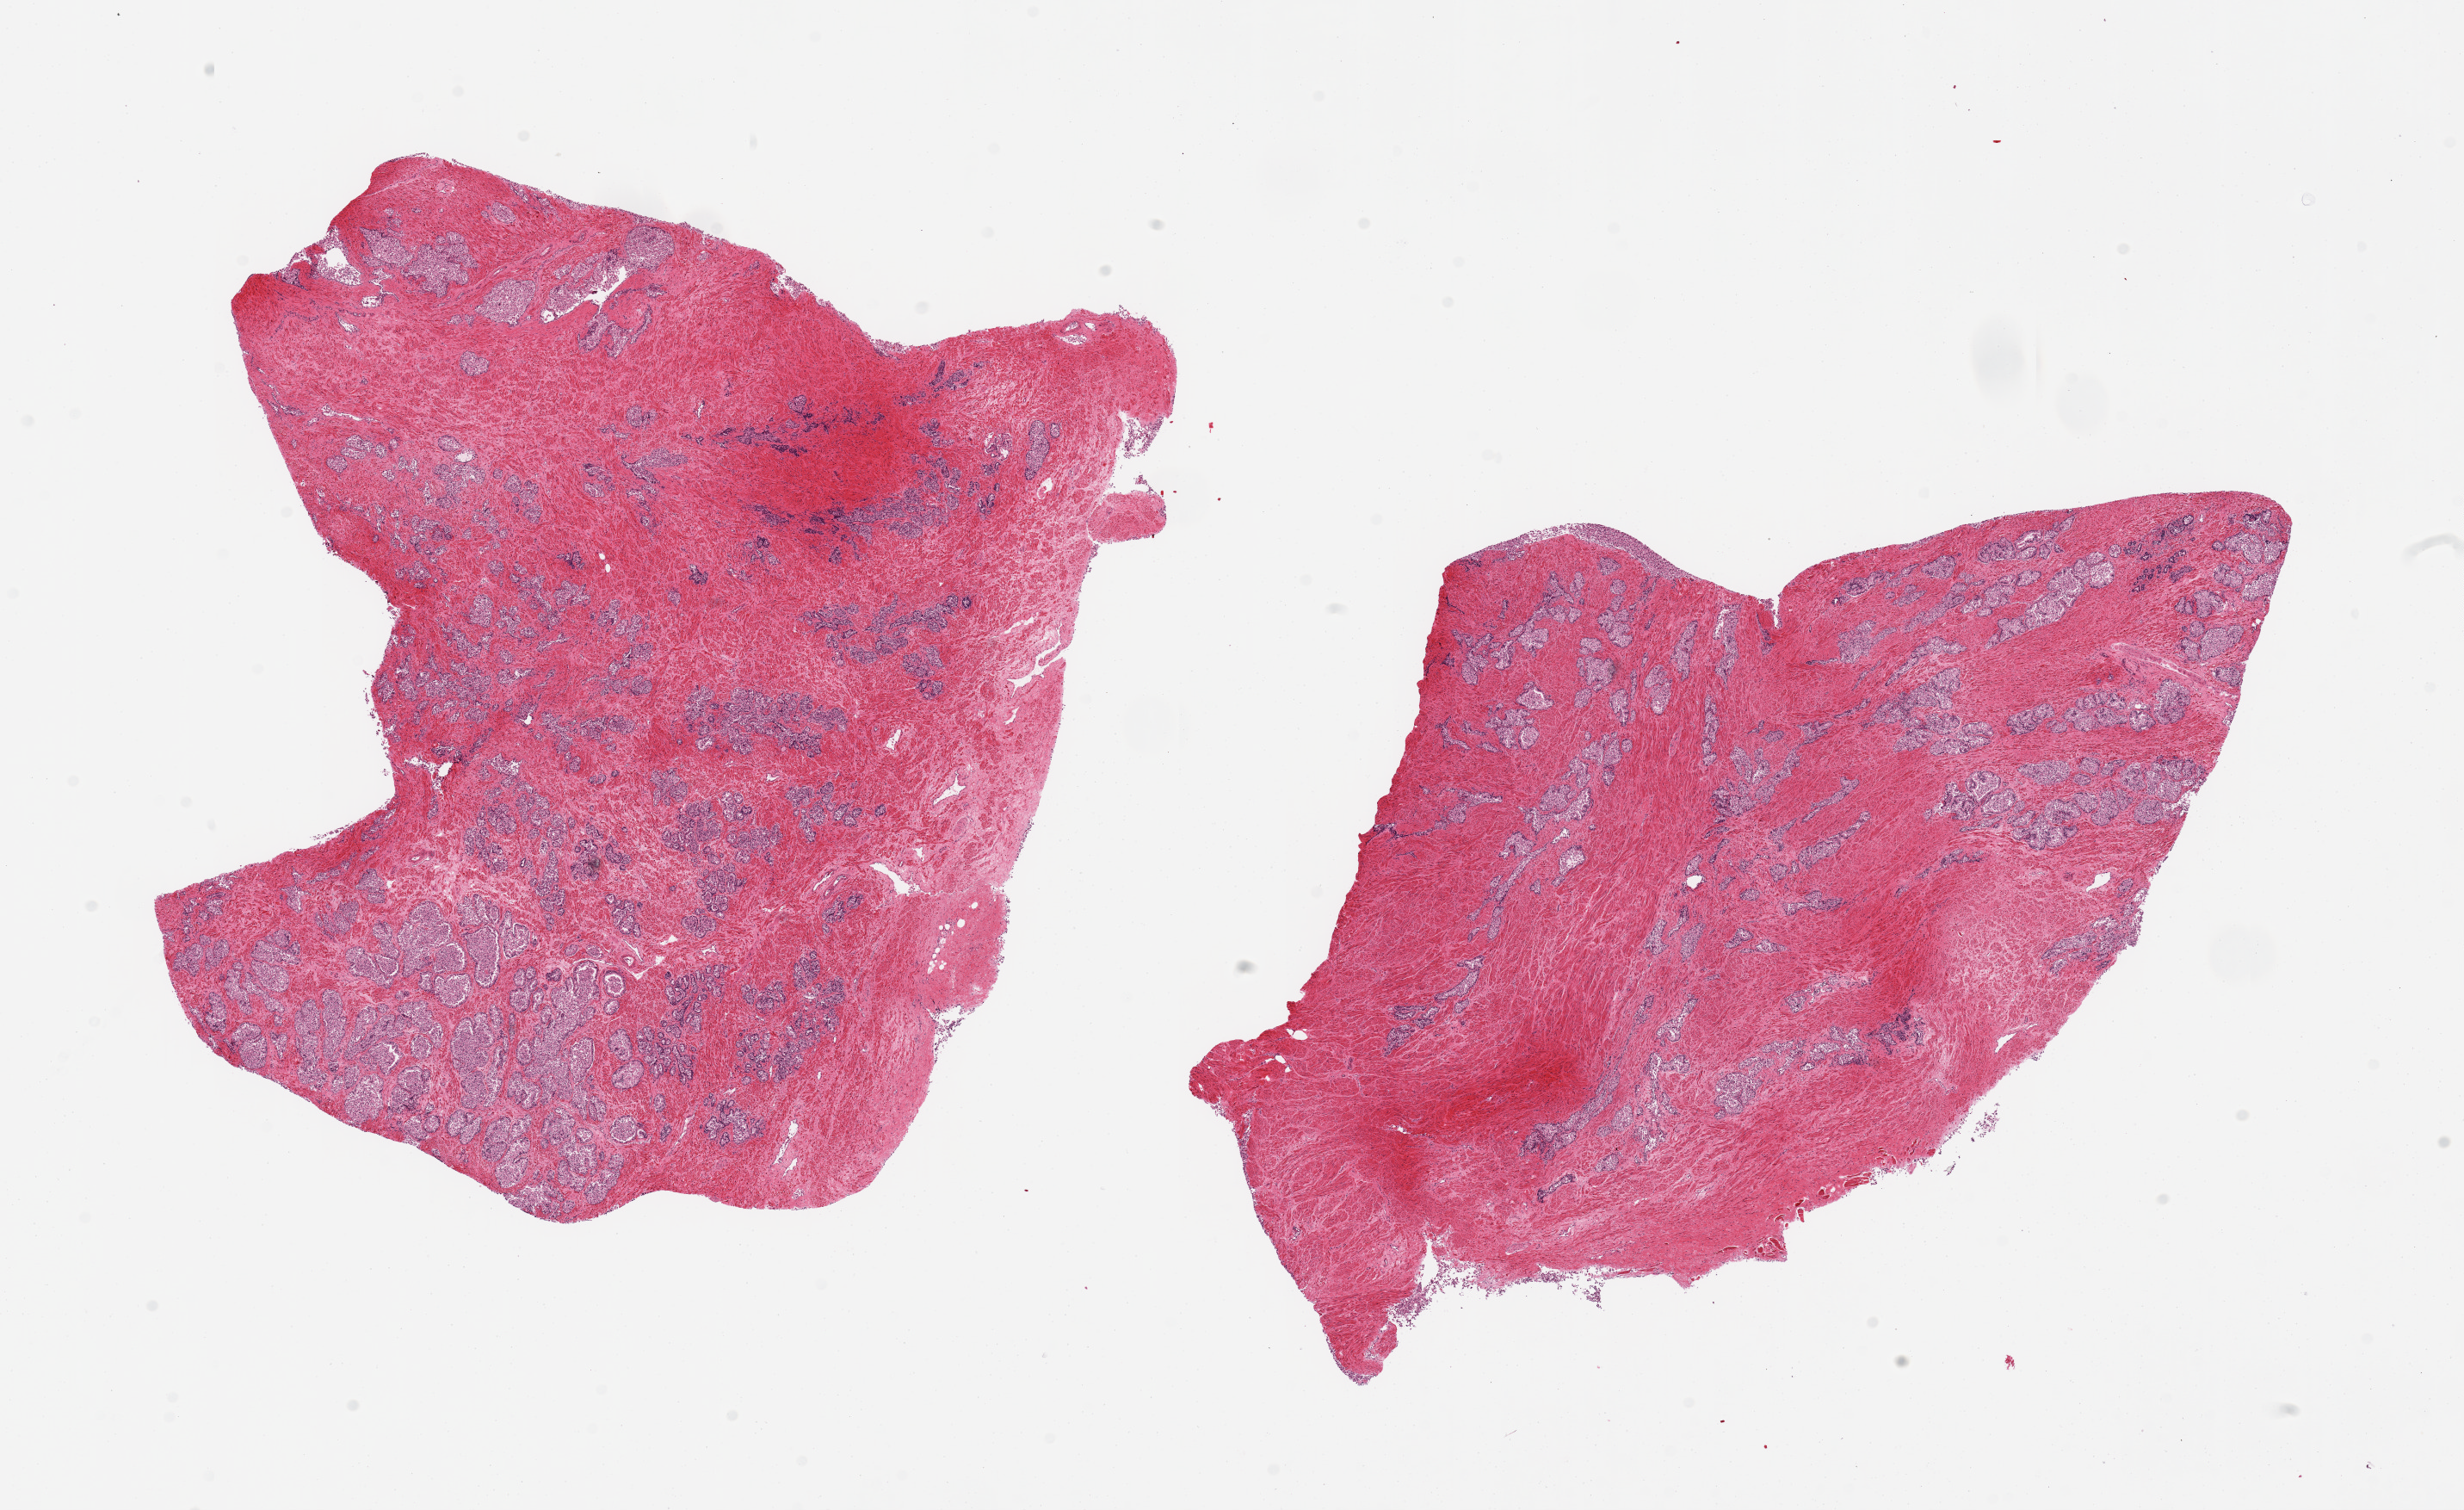
Whole-slide image, hematoxylin and eosin (H&E) stain, brightfield — shown as a low-resolution overview of the whole scanned area (about 22.6 x 13.9 mm), PAXgene-fixed, paraffin-embedded tissue, section of prostate (target tissue), tissue donor sample. Donor: male.
• review note (as recorded): 2 pieces, epithelium sloughing